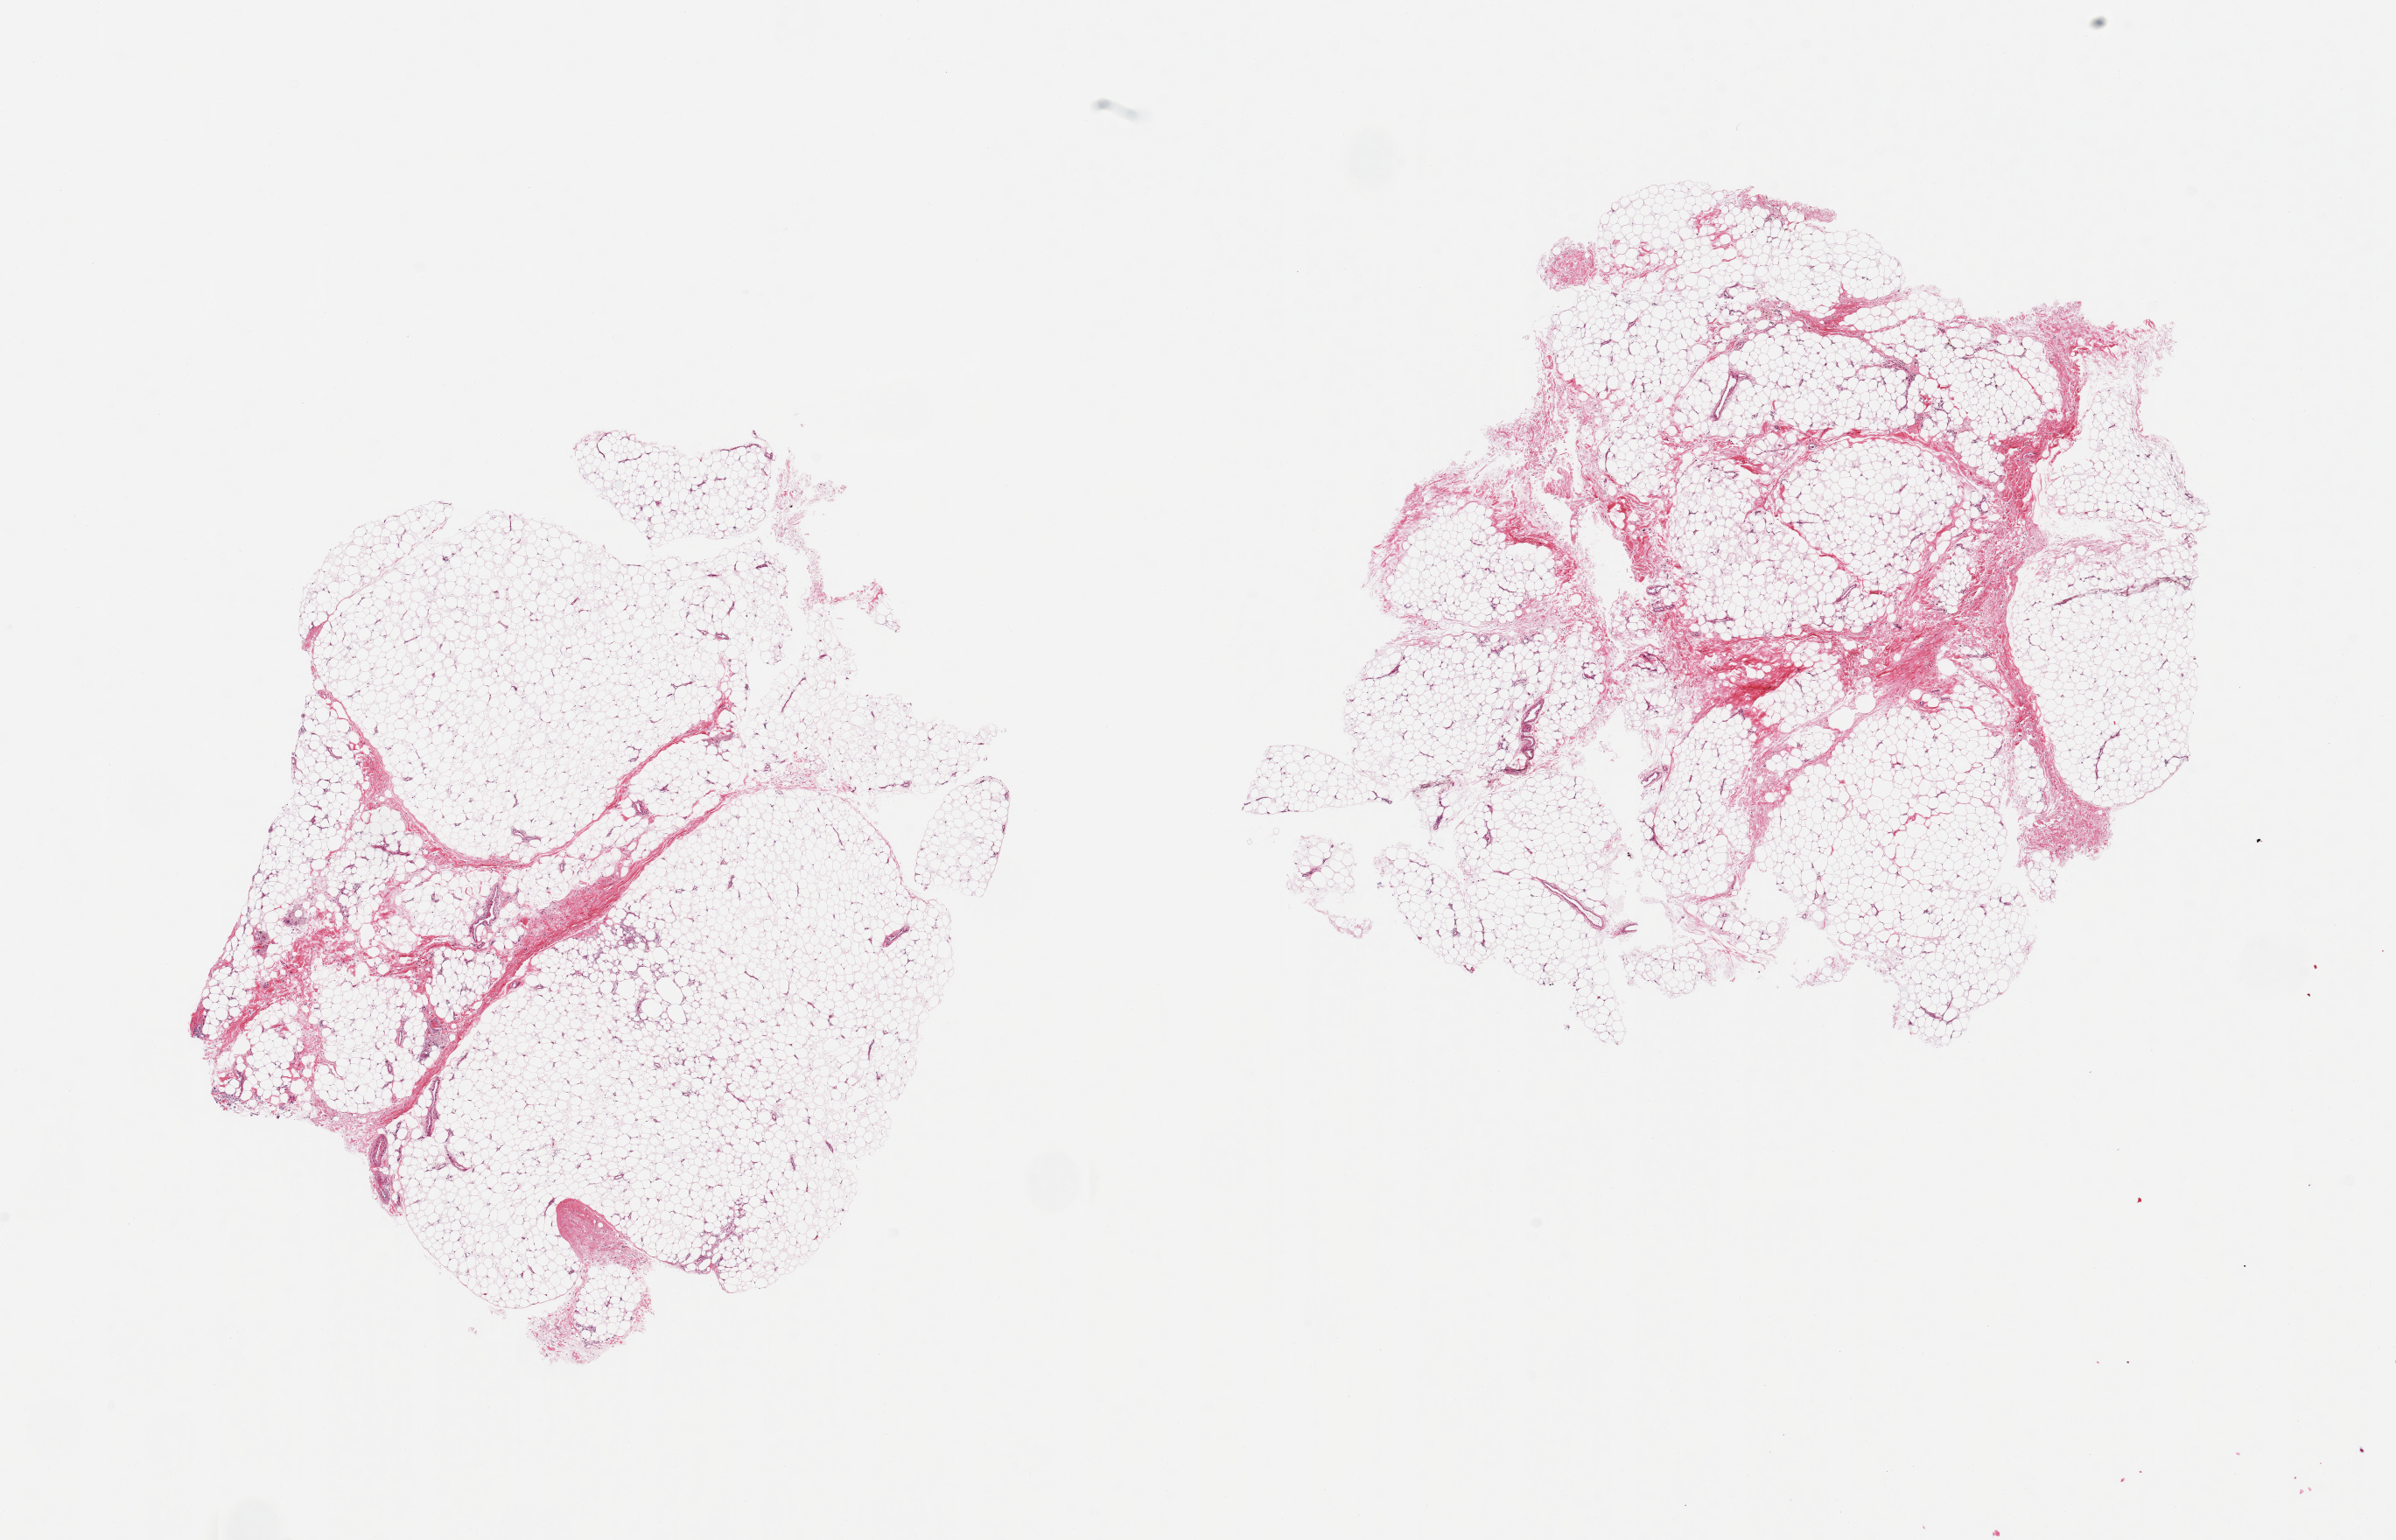
Whole-slide image, haematoxylin and eosin stain — low-resolution overview of the scanned area, about 21.7 x 13.9 mm, PAXgene-fixed, paraffin-embedded tissue, sampled site (target tissue): adipose tissue, donor tissue sample. Male donor.
Pathologist's review note for this sample: 2 pieces; 5% fibrous content.